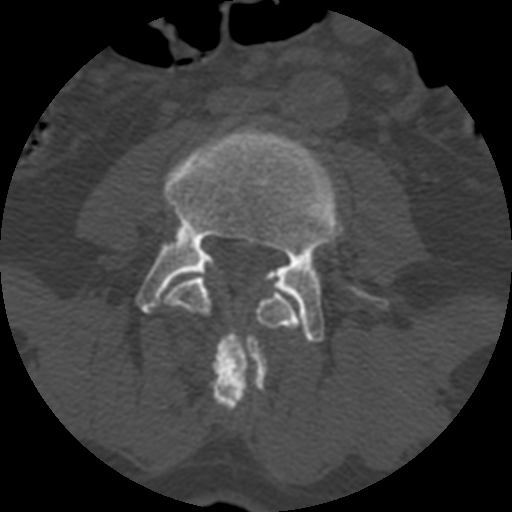
CT including the spine, one axial slice; position 290 of 399 along the scan axis; reconstruction kernel STANDARD; 120 kVp; bone window (W 1800 / L 400 HU); 512 × 512 image matrix, field of view 160 × 160 mm. Patient age 71 years. From the clinical record (not read from this slice): primary cancer: prostate.
Annotated regions visible in this slice (semi-automatically segmented with operator editing):
- L3 vertebra: bounding box <165,274,301,411> (left, top, right, bottom; pixels)
- L4 vertebra: <136,126,388,343>